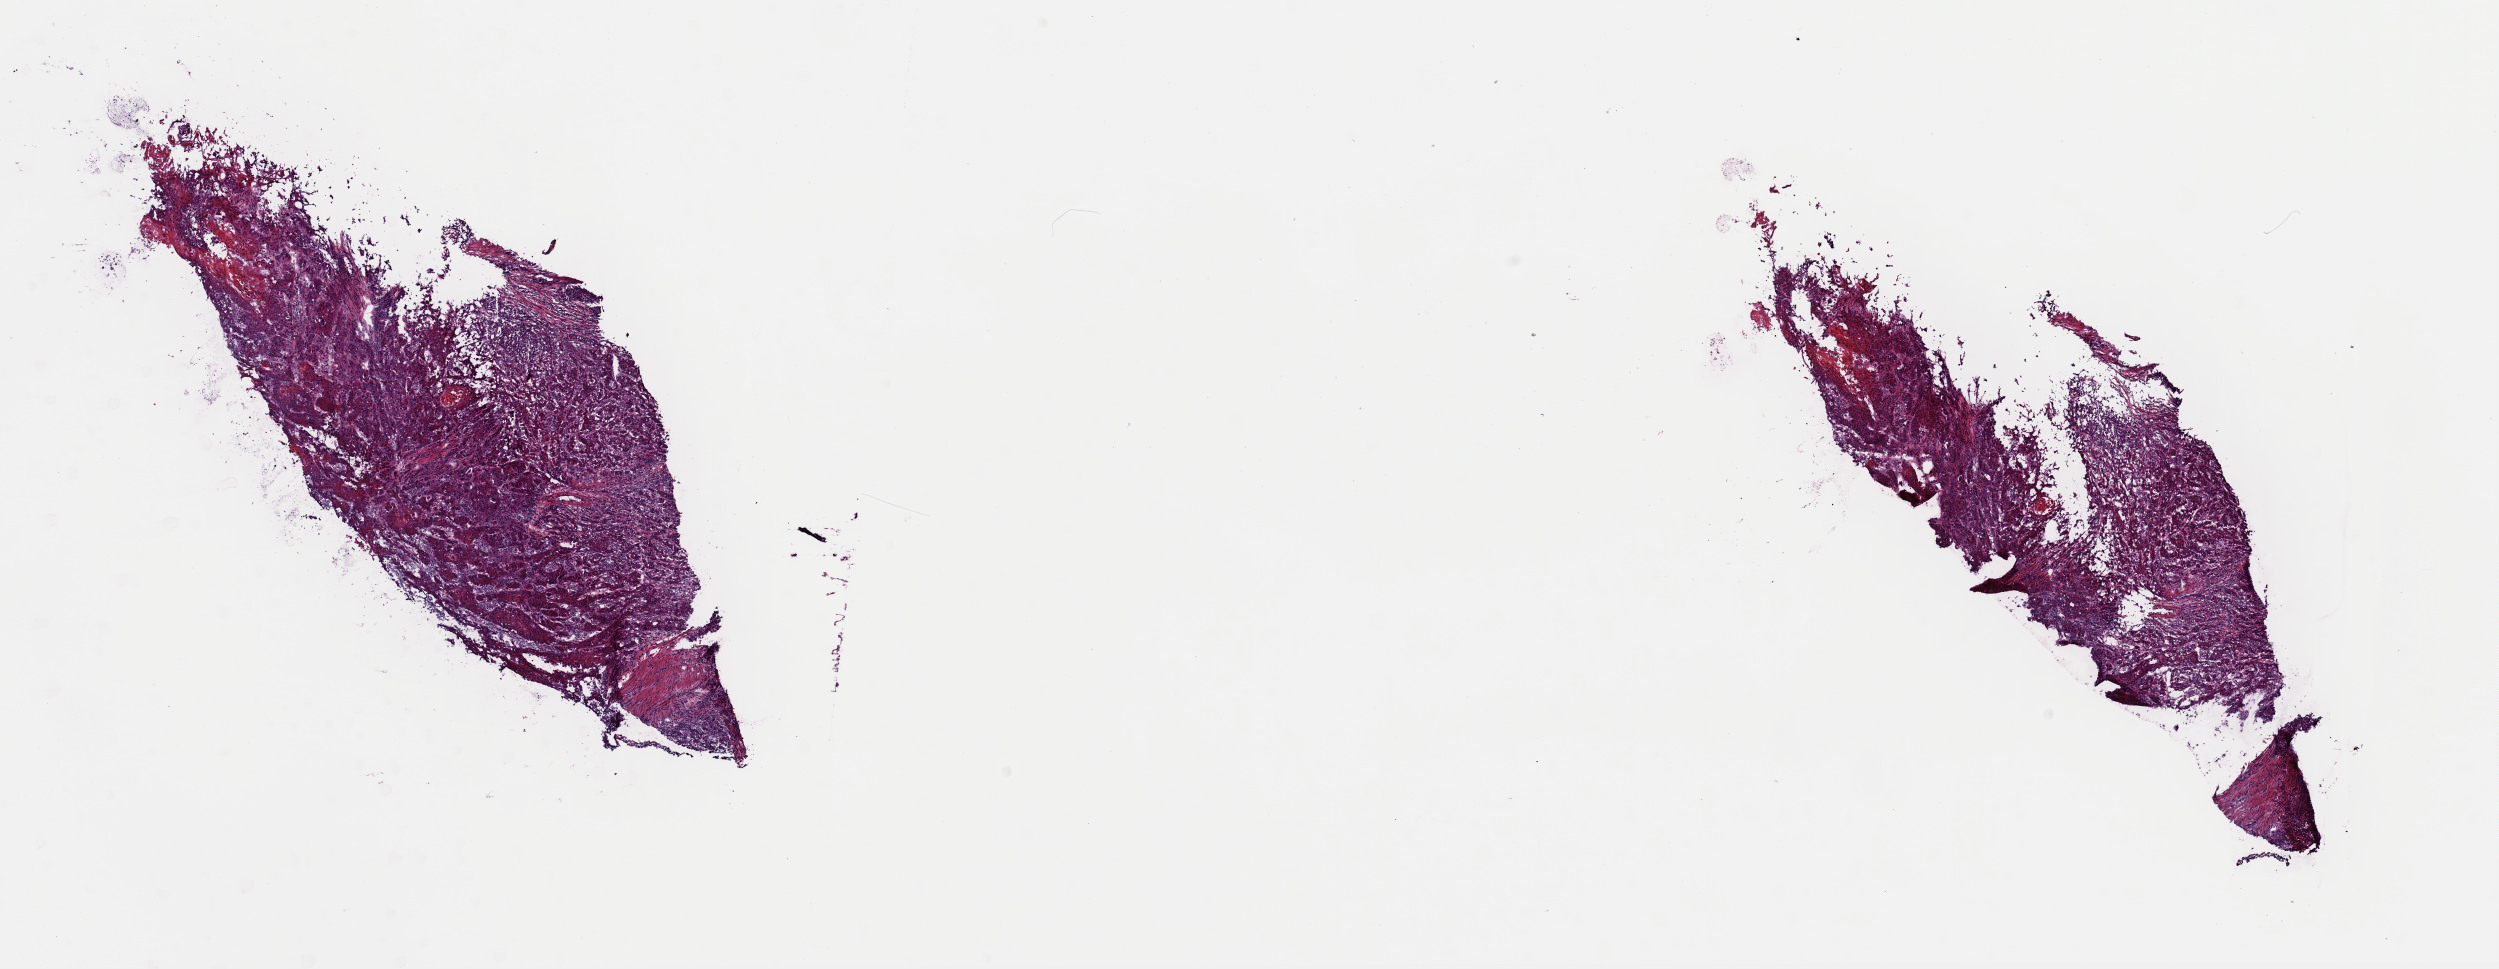
H&E-stained whole-slide image — whole scanned area (about 19.7 x 7.7 mm, from a 40x scan) shown as a low-resolution overview. Frozen section. Primary tumour sample from the esophagus. Patient: male, age at initial diagnosis 47 years. Histologic grade: G3 (poorly differentiated). Composition of this section per pathologist review: tumour cells 75%, tumour nuclei 75%, normal cells 0%, stromal cells 23%, necrosis 2%. Inflammatory infiltration, as recorded: lymphocyte infiltration 3%, monocyte infiltration 2%, neutrophil infiltration 2%.
* diagnosis: Squamous cell carcinoma, NOS (middle third of esophagus)
* AJCC pathologic stage: IIA (6th edition)